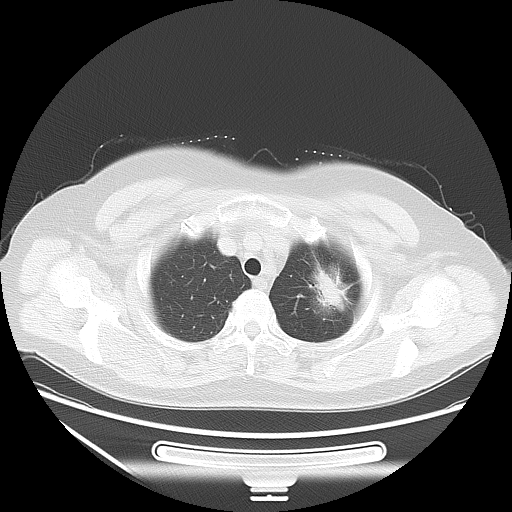
Chest CT, one axial slice; position 47 of 53 along the scan axis; 120 kVp; lung window (W 1500 / L -600 HU); 5 mm slice thickness; 512 × 512 image matrix, field of view 403 × 403 mm. Female patient, age 66 years. From the clinical record (not read from this slice): clinical TNM (as recorded): T2 N0 M0; histopathological grade: G2.
Outlined on this slice (bounding box drawn by a radiologist):
- lung tumour (recorded histology: adenocarcinoma): box from (x=298, y=253) to (x=363, y=324) px